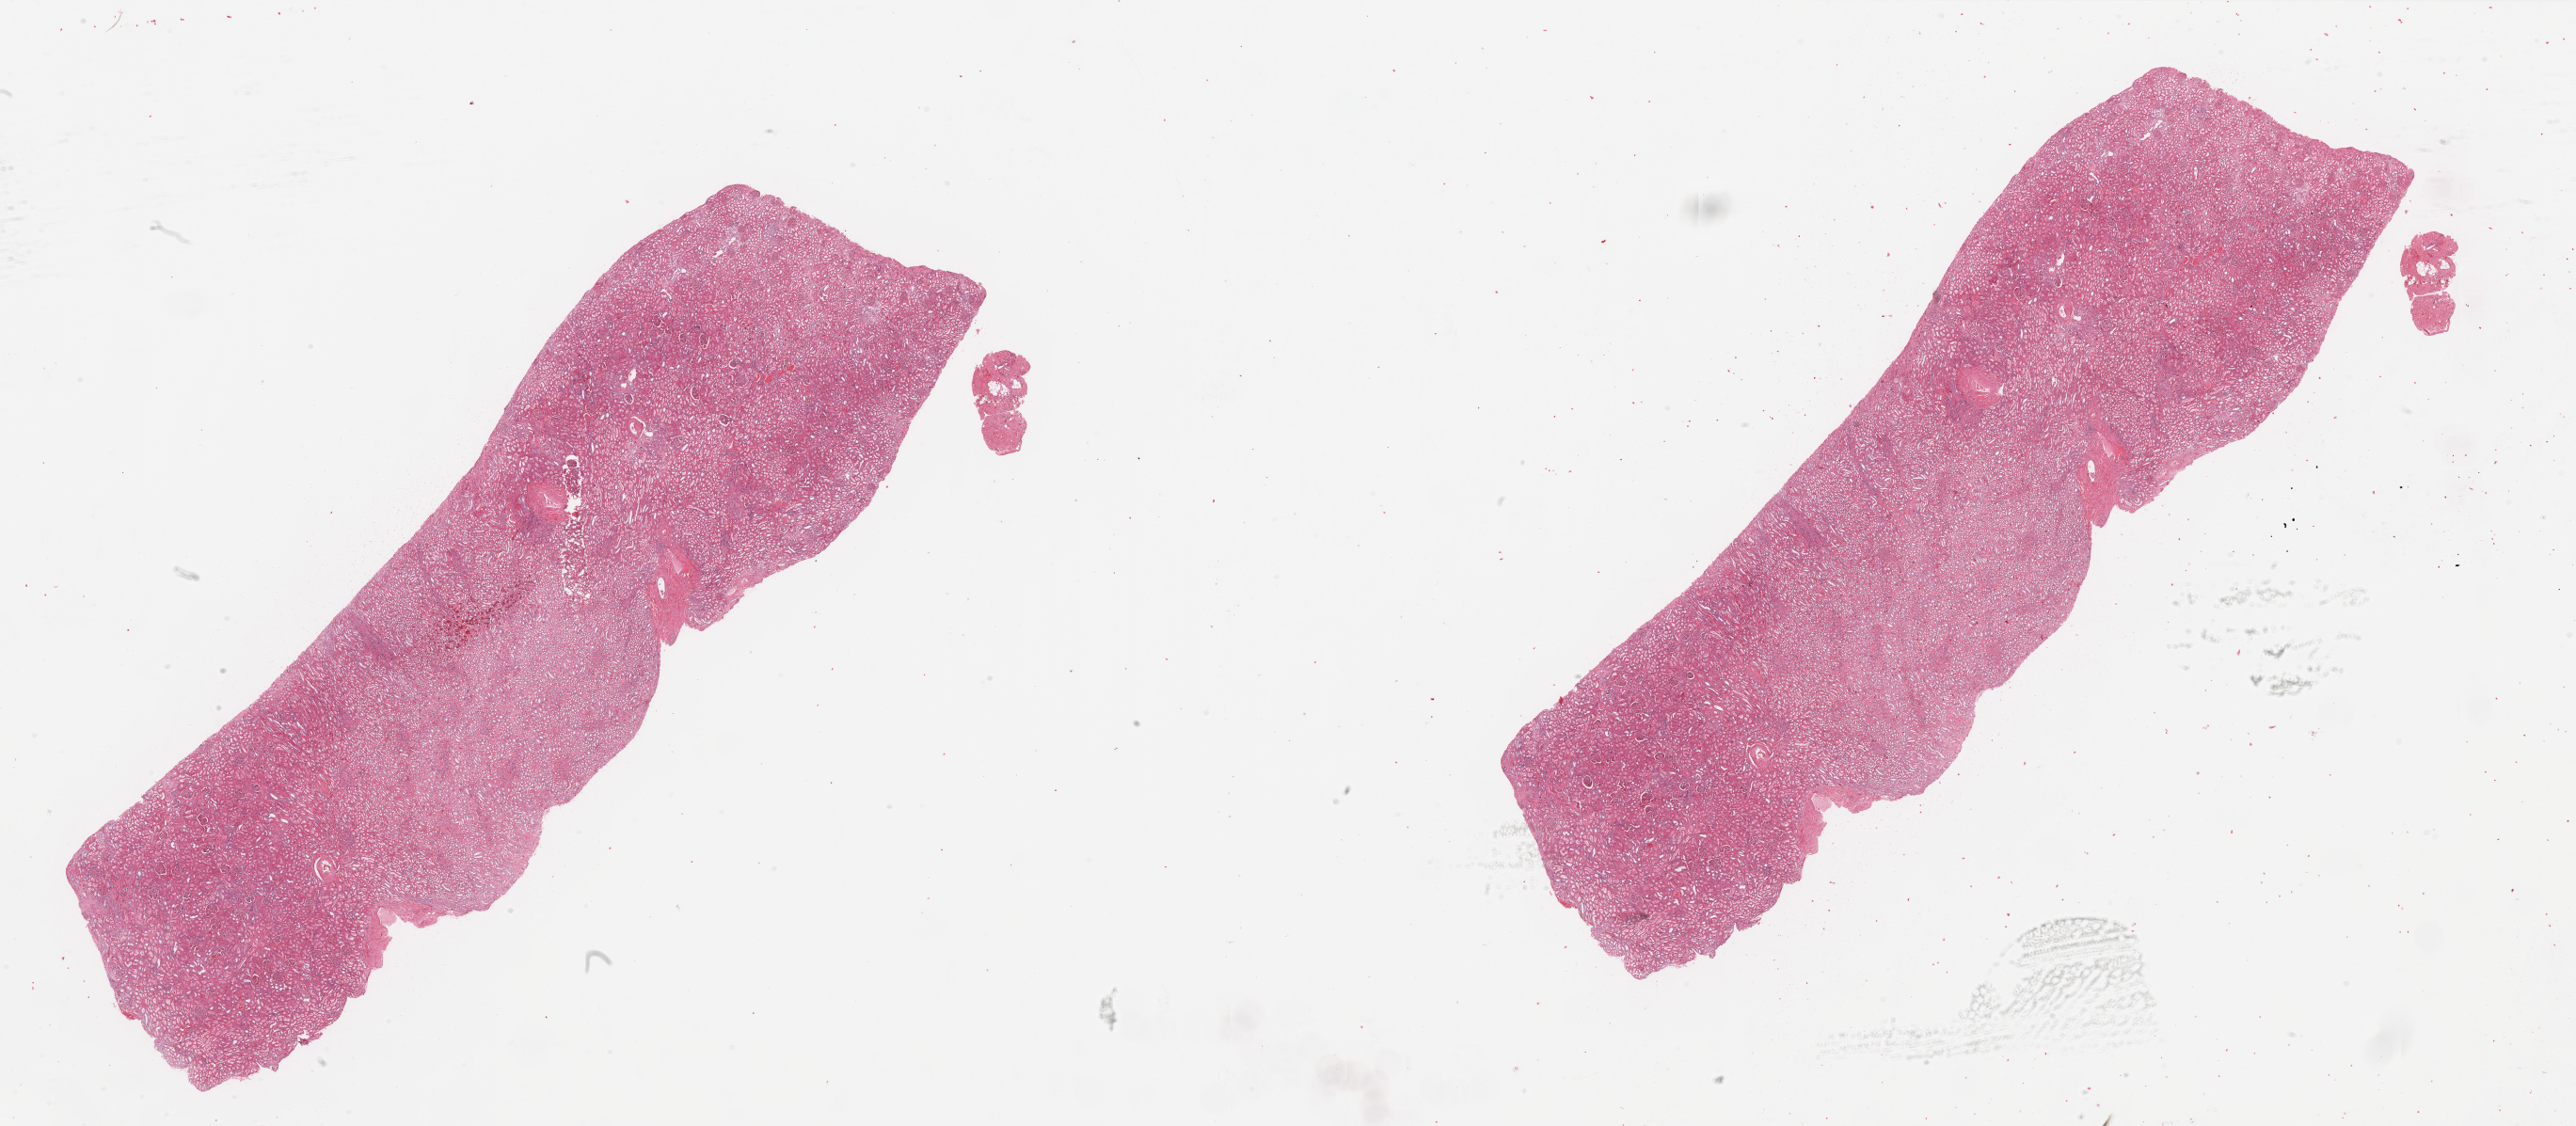
Digitized H&E-stained tissue section (whole slide) — a low-resolution overview of the entire scanned area, about 43.3 x 18.9 mm (from a 20x scan). Normal (non-tumour) tissue sample, kidney. 66-year-old female patient.
This section: normal (non-tumour) tissue from the same patient. Patient diagnosis: Renal cell carcinoma, NOS.